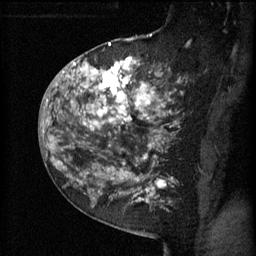
Breast MRI (dynamic contrast-enhanced), one sagittal slice. Slice 36 of 60 in the series (ordered by position). 3 images stored at this slice position (order not interpretable as contrast timing). 1.5 T. TE 4.2 ms, TR 11 ms. 2 mm slice thickness. 256 × 256 image matrix, field of view 180 × 180 mm. Patient: female, 52 years.
Annotated regions visible in this slice (semi-automatic segmentation, software-assisted and operator-edited):
- analysis volume of interest (the breast-tissue region the enhancement analysis was run in; not a lesion): box from (x=81, y=52) to (x=174, y=157) px
- tumour enhancement mask (voxels above the 70 % enhancement threshold inside the analysis volume of interest): (x=81, y=56)–(x=172, y=157)